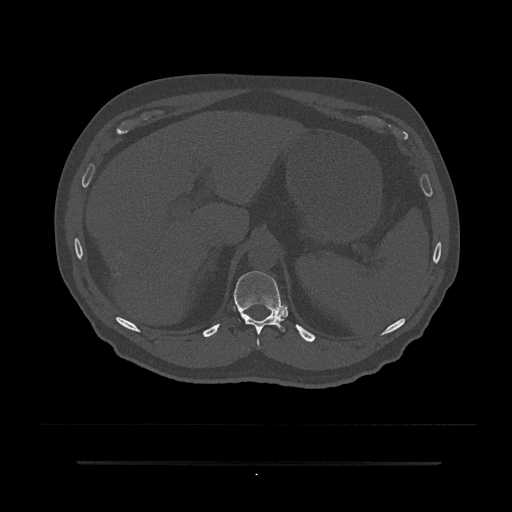
CT including the spine, one axial slice; 120 kVp; bone window (W 1800 / L 400 HU); 0.5 mm slice thickness; 512 × 512 image matrix. Male patient, age 59 years. From the clinical record (not read from this slice): primary cancer: bile ducts; vertebrae with lytic lesions (as recorded): T10.
Outlined on this slice (semi-automatically segmented with operator editing):
- T11 vertebra: bounding box [x1, y1, x2, y2] px = [234, 271, 285, 347]